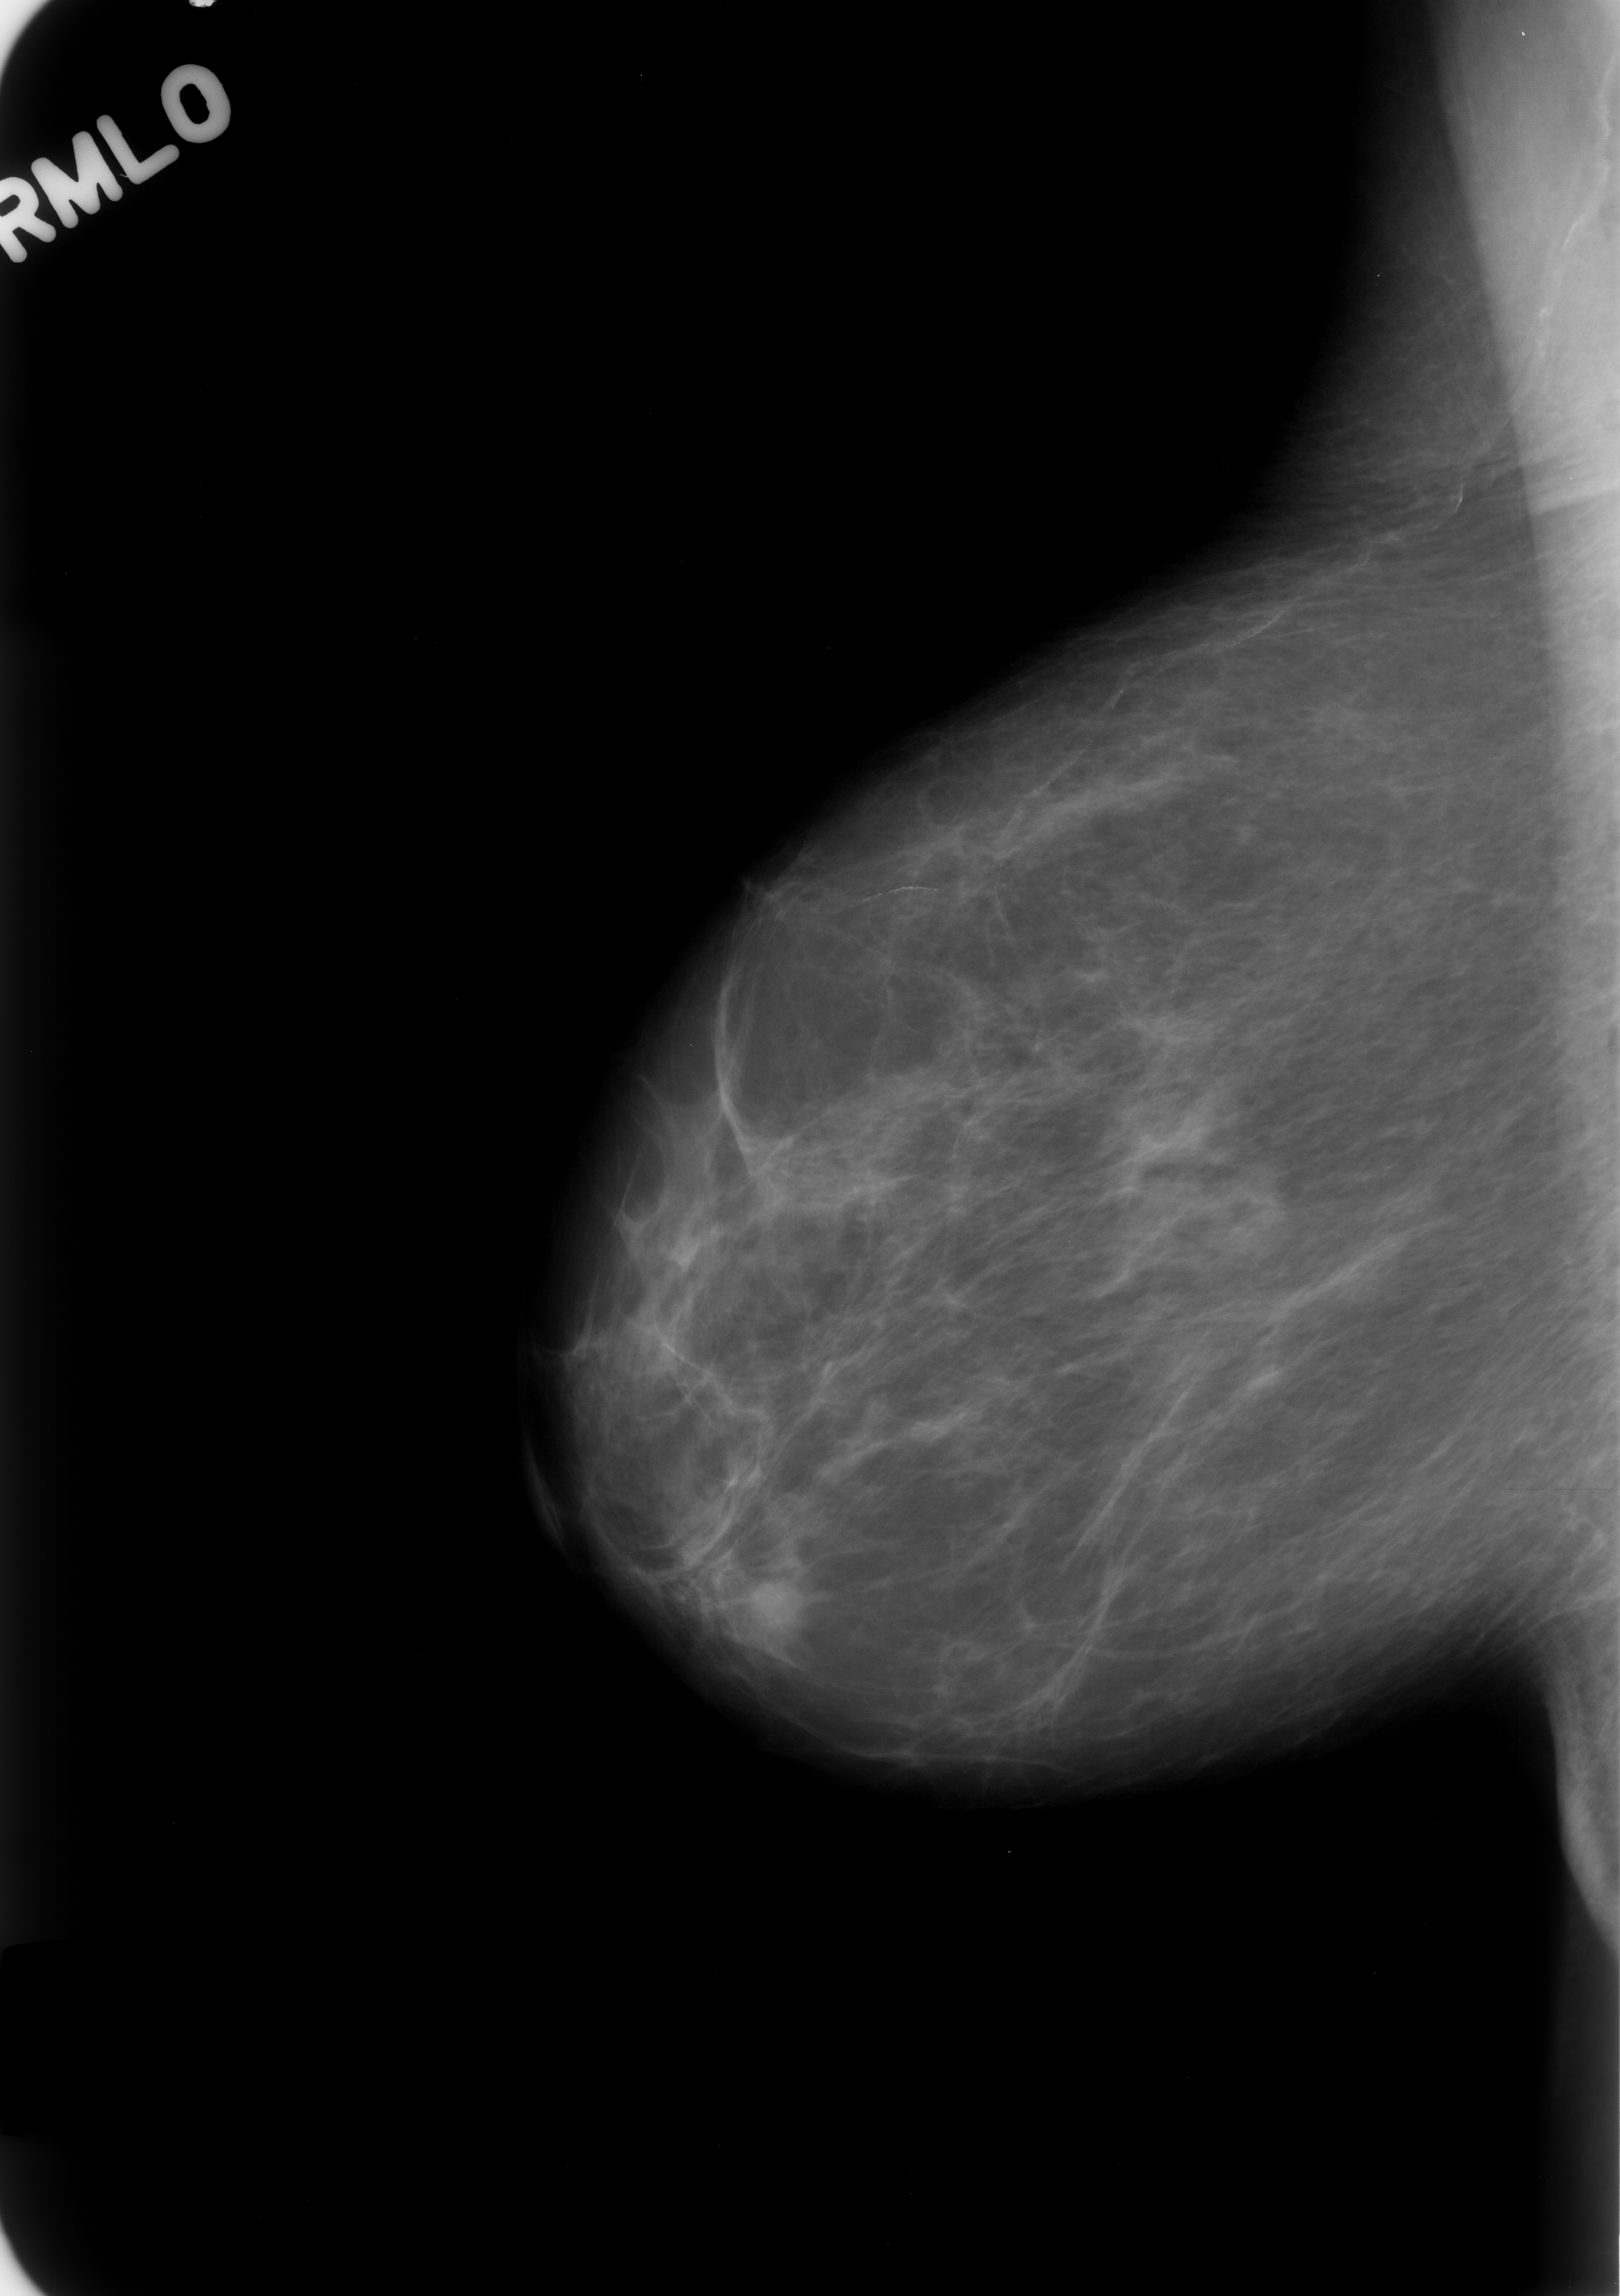
Digitized screen-film mammogram. Right breast. Mediolateral oblique (MLO) view. Breast composition: almost entirely fatty (BI-RADS density category 1 of 4). 1620 × 2296 image matrix.
Expert-marked regions of interest on this image (one box per marked abnormality):
- mass, shape round, margins microlobulated; BI-RADS assessment category 3; subtlety rating 5 on a 1 (subtle) to 5 (obvious) scale; benign; no additional work-up was recommended (outcome (as recorded, no biopsy): benign without callback): bounding box [x1, y1, x2, y2] px = [701, 1561, 827, 1662]